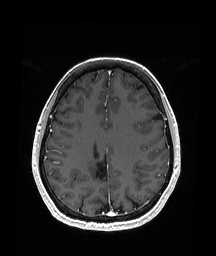
Brain MRI from a brain-tumour surgery series, one axial slice; position 71 of 151 along the scan axis; T1-weighted post-contrast; 1.05 mm slice thickness; 216 × 256 image matrix, field of view 211 × 250 mm. Case-level facts recorded for this patient, not image findings: histopathology: Oligodendroglioma; WHO grade: 2; IDH mutation: yes.
Annotated regions visible in this slice (manually delineated by an expert):
- previous resection cavity: bounding box <94,149,109,175> (left, top, right, bottom; pixels)